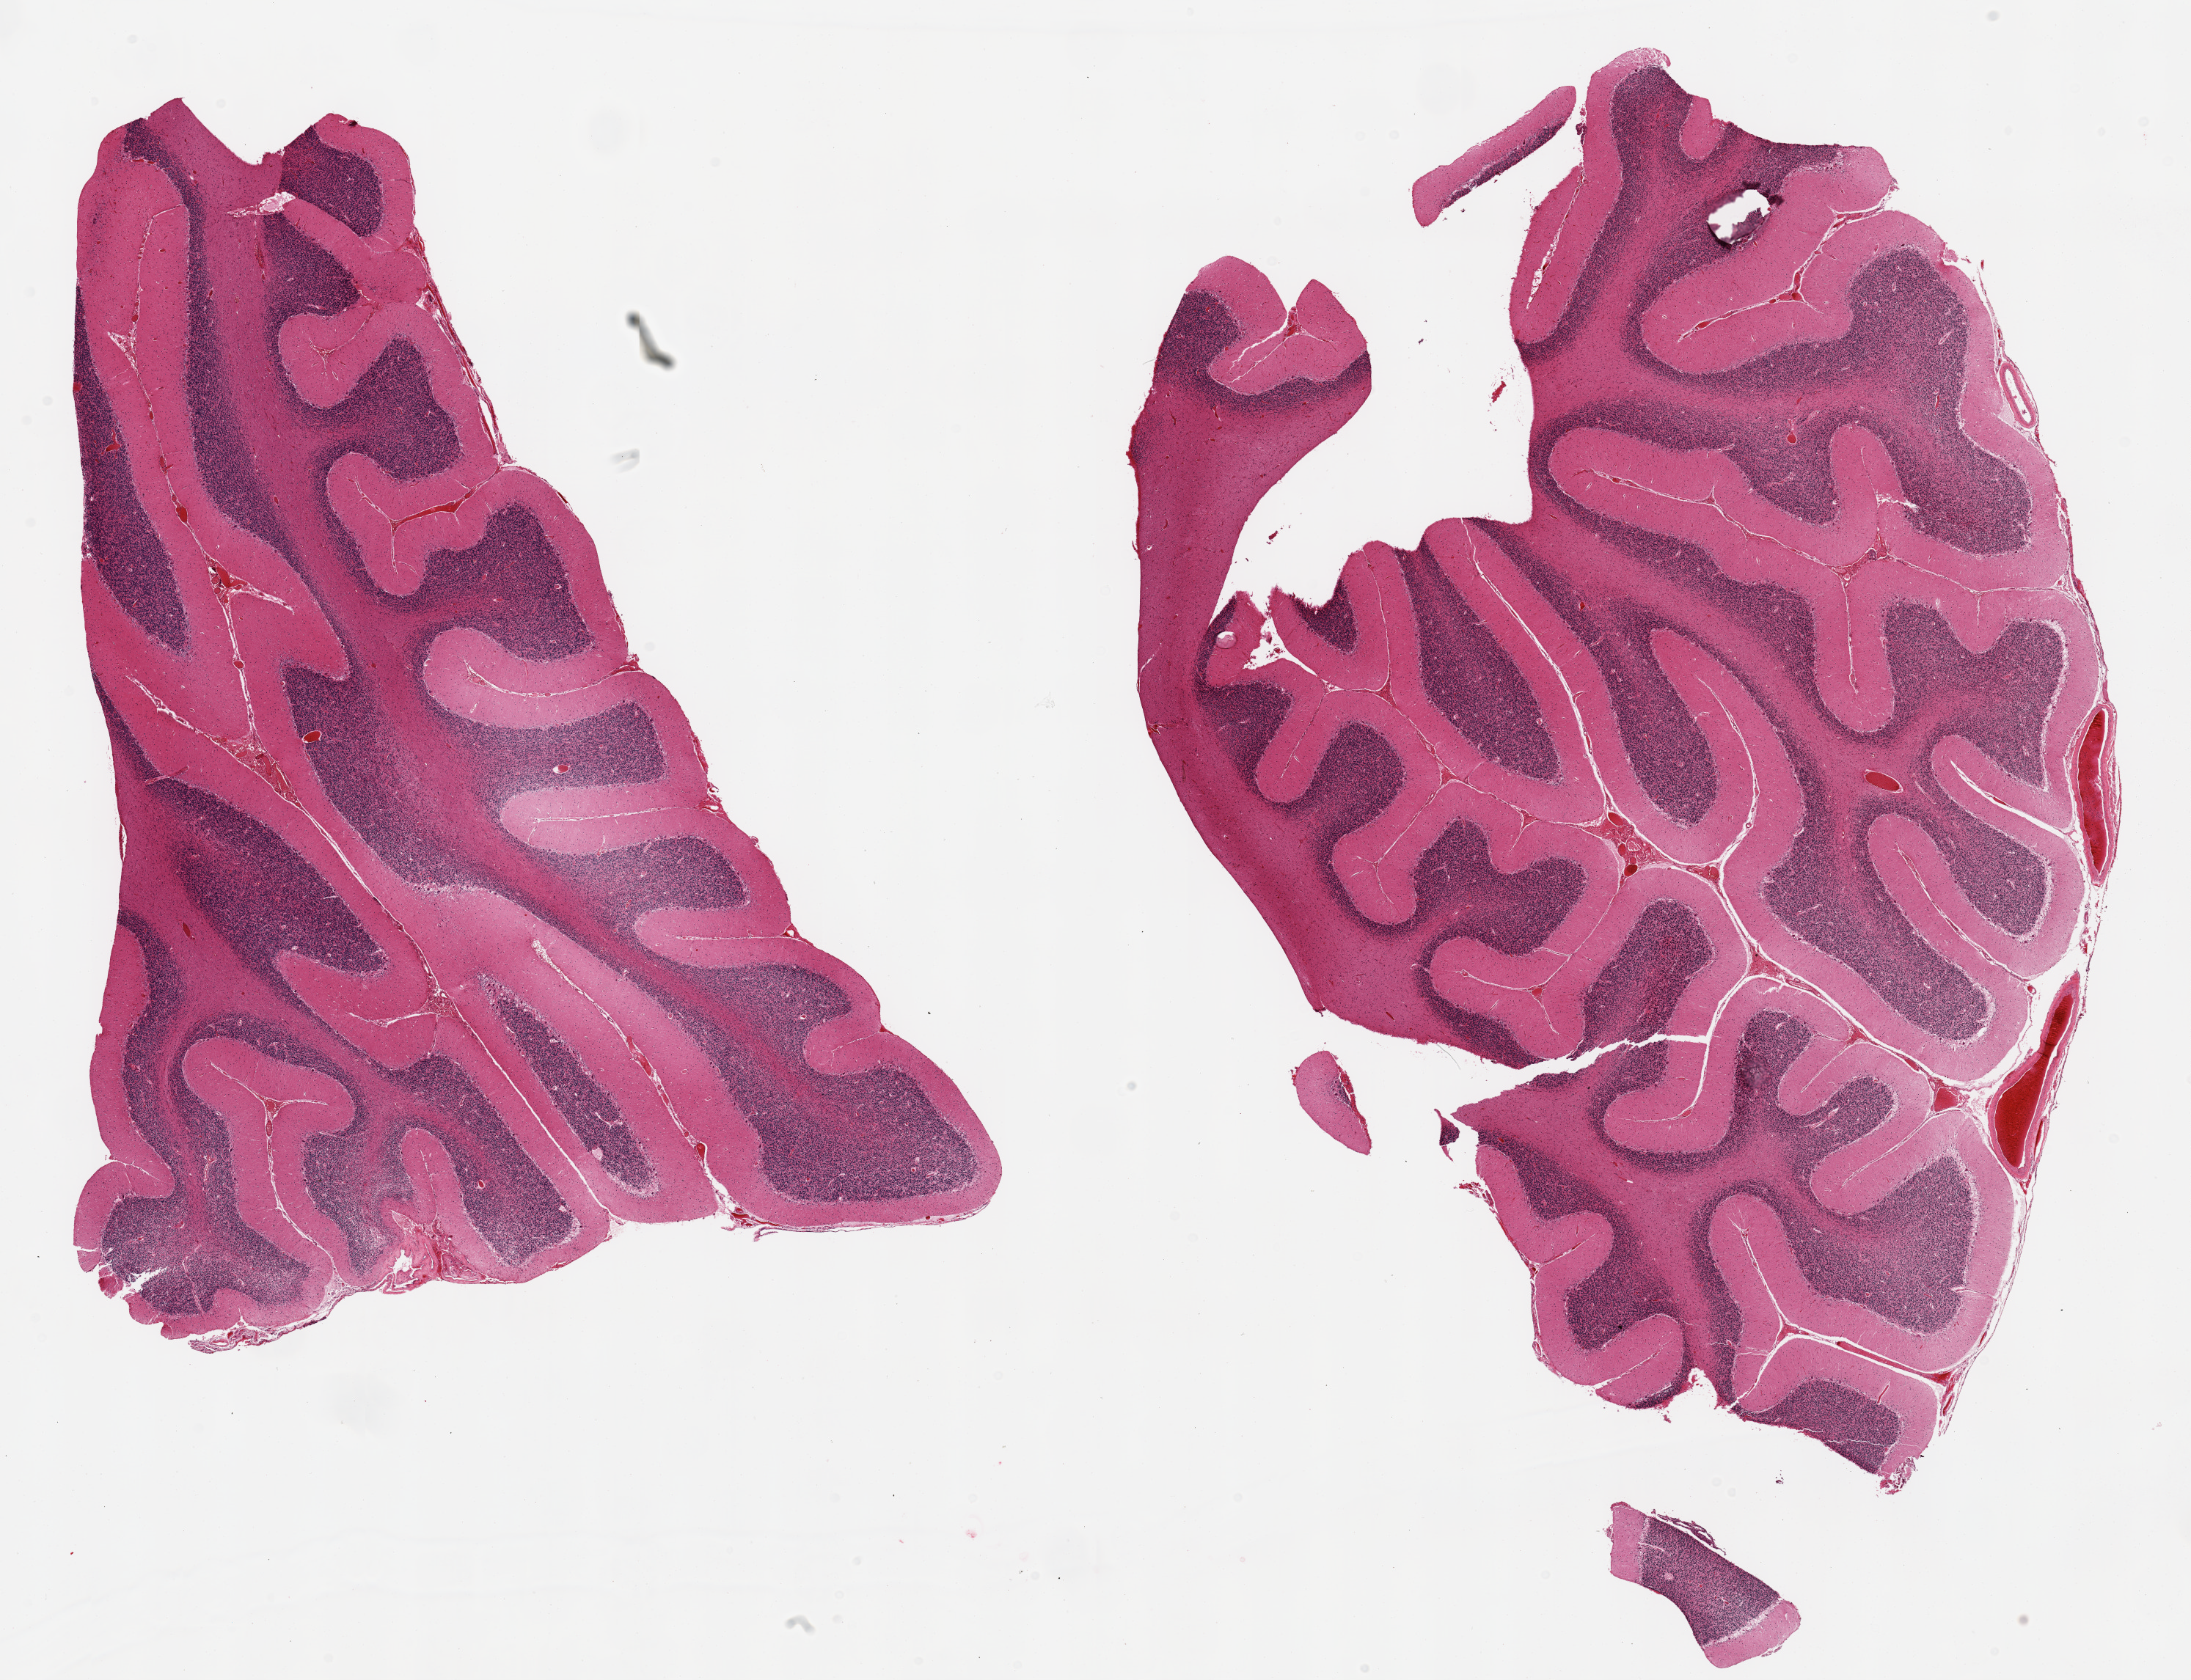
Digitized haematoxylin and eosin-stained section — a low-resolution overview of the entire scanned area, about 23.6 x 18.1 mm; PAXgene-fixed paraffin-embedded (PFPE) section; sampled site (target tissue): cerebellum; tissue donor sample. Male donor.
* reviewer comment on this tissue sample: 2 pieces; Purkinje cells well visualized with no clear evidence of hypoxic damage